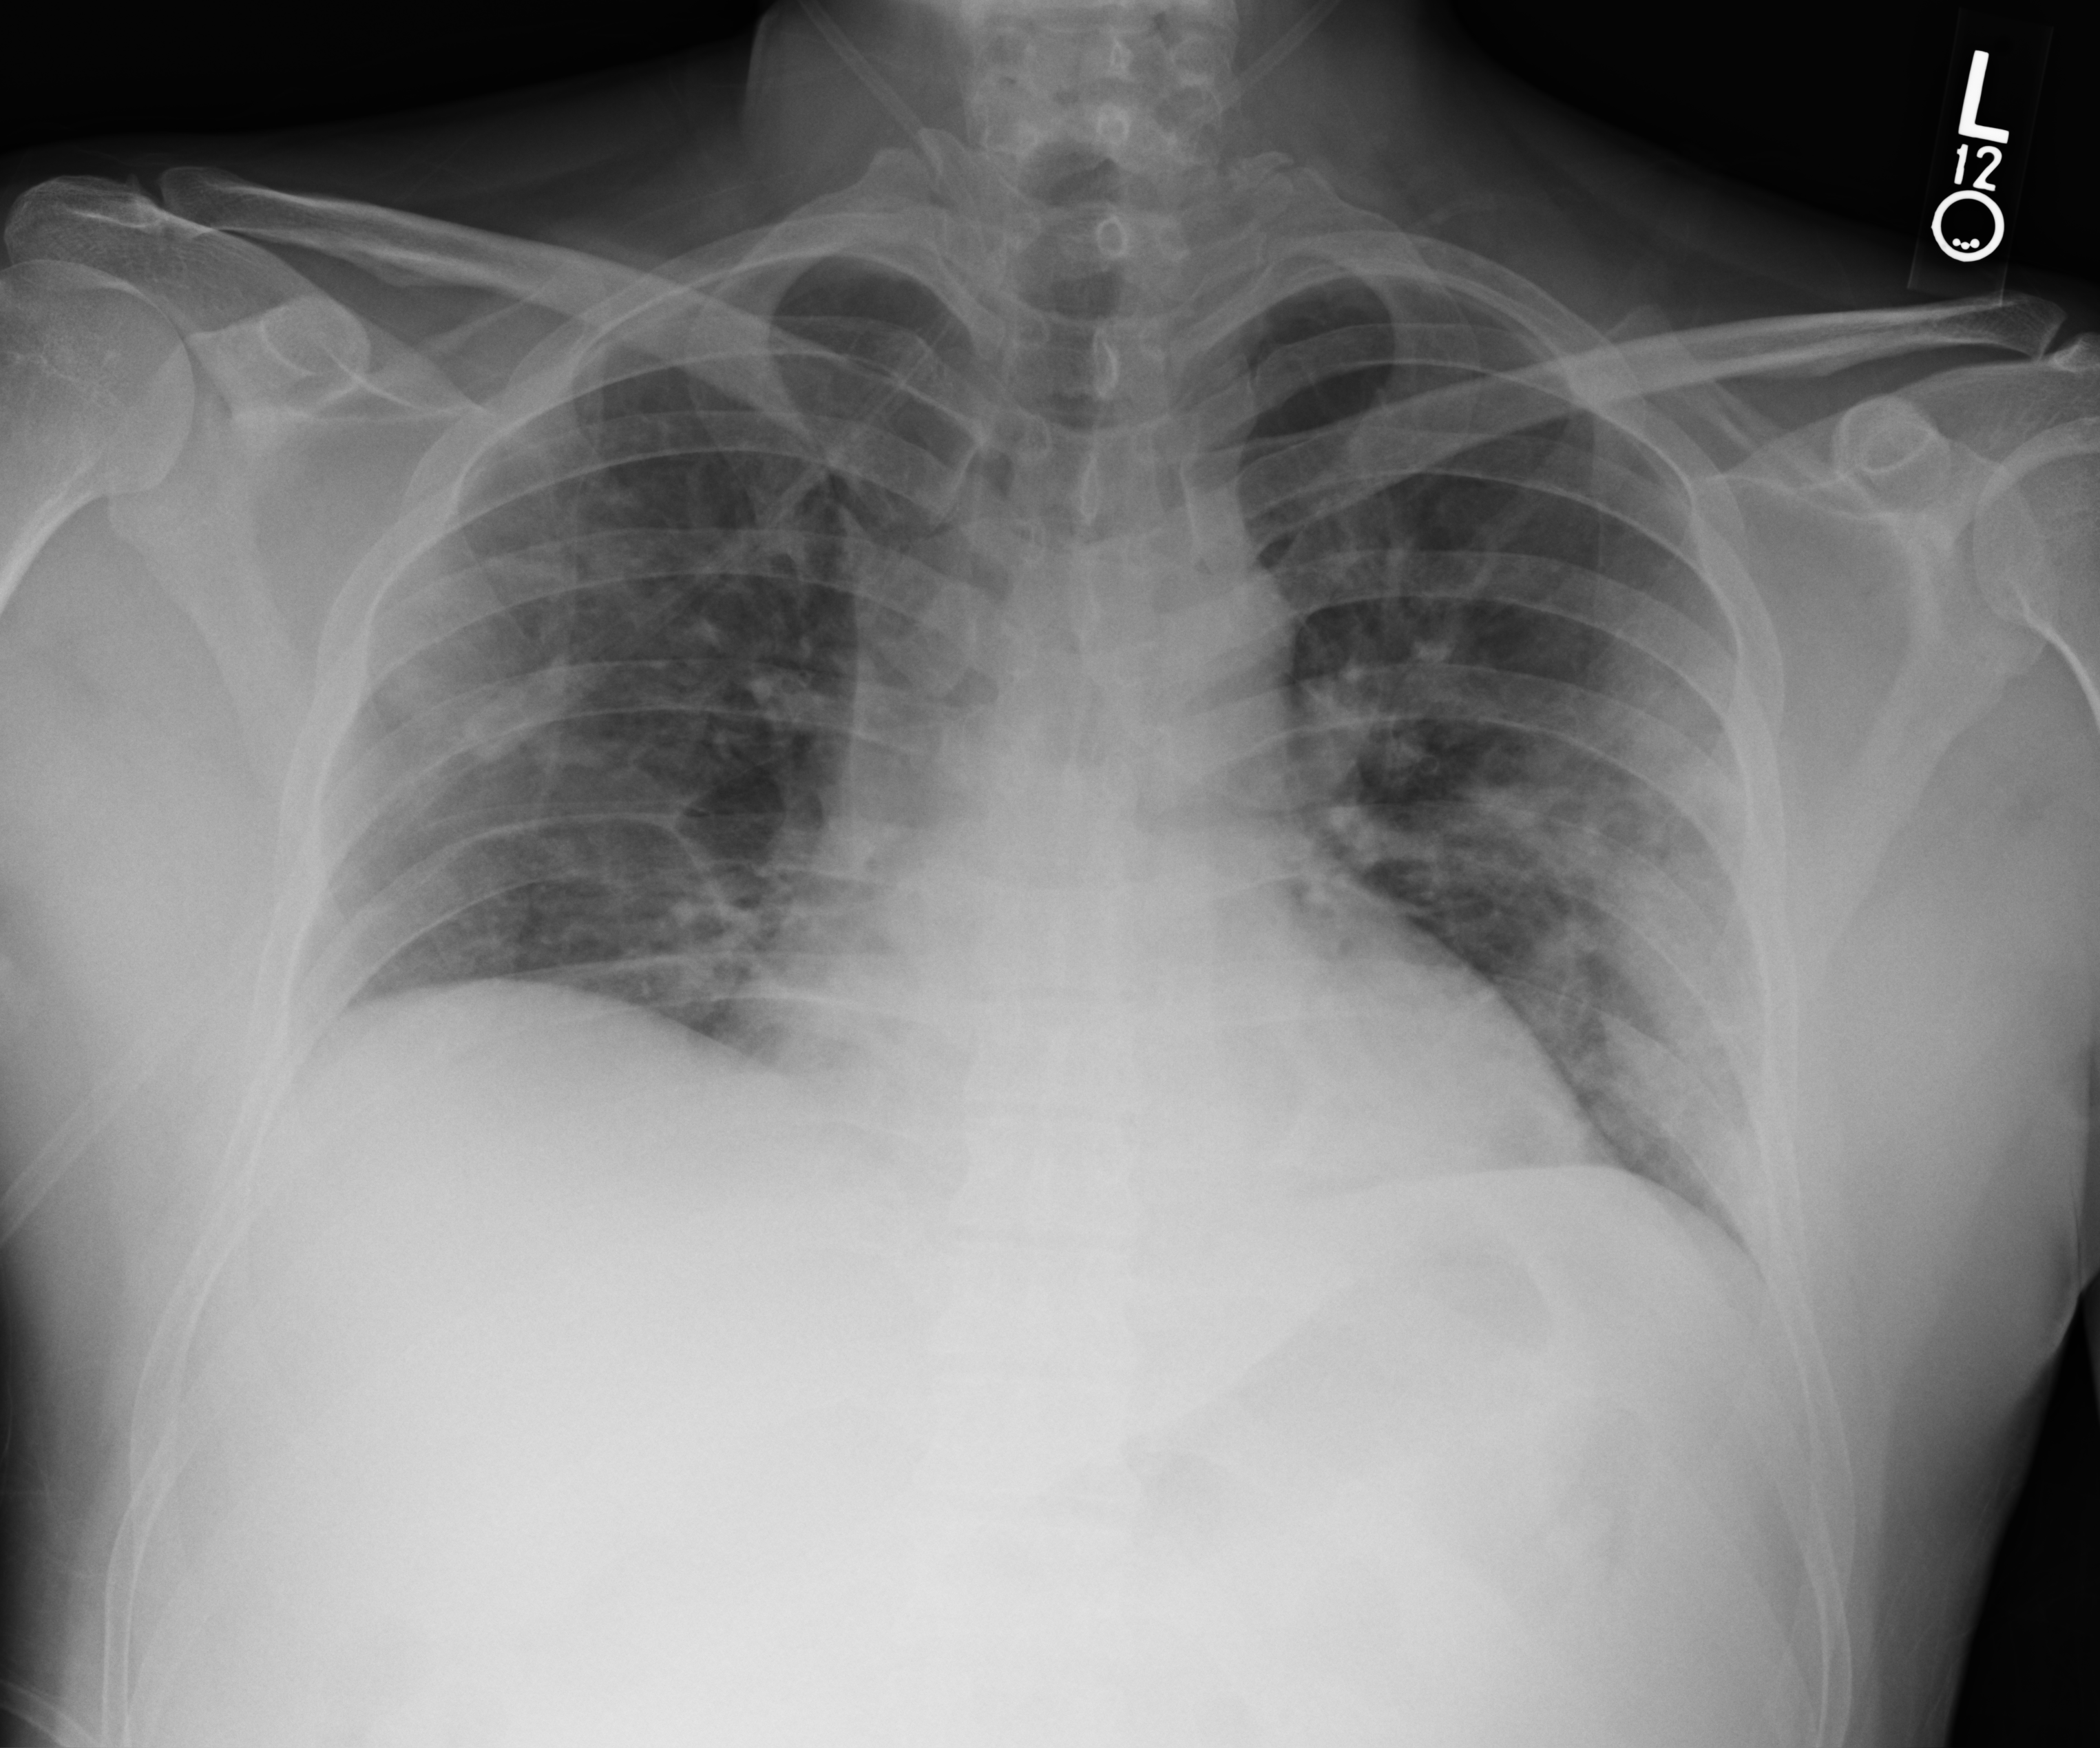
Bedside chest radiograph (computed radiography). Patient hospitalised with COVID-19; male, aged 18–59 years.
From the hospital-stay record, not from the radiograph (when in the stay this image was taken is not recorded): smoking status (admission record): never; mechanically ventilated during this hospital stay: no.